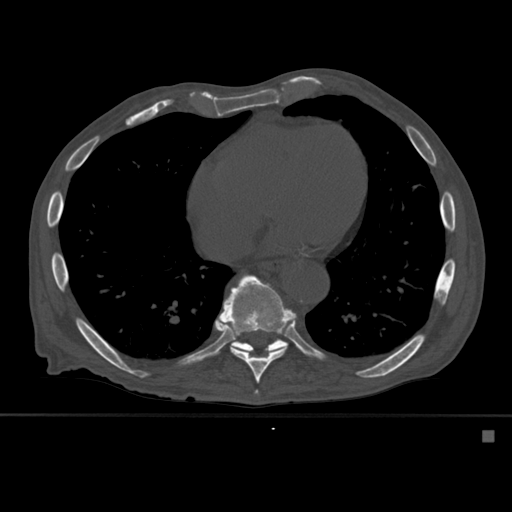
CT including the spine, one axial slice; position 328 of 527 along the scan axis; bone window (W 1800 / L 400 HU); 512 × 512 image matrix, field of view 373 × 373 mm. Patient: male, 78 years. From the clinical record (not read from this slice): primary cancer: prostate.
Annotated regions visible in this slice (semi-automatically segmented with operator editing):
- T10 vertebra: bounding box [x1, y1, x2, y2] px = [231, 338, 286, 353]
- T8 vertebra: [255, 390, 258, 394]
- T9 vertebra: [219, 273, 297, 383]